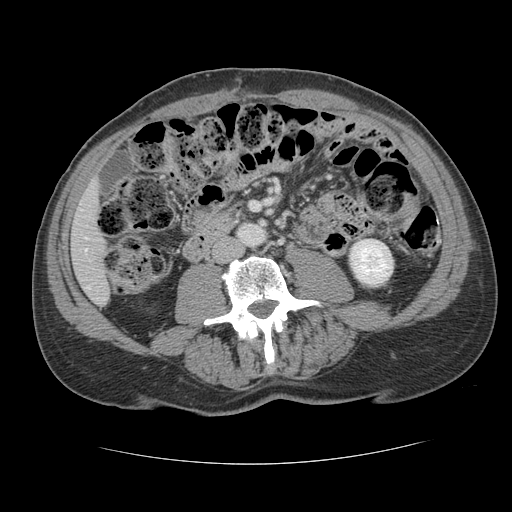
Contrast-enhanced abdominal CT, one axial slice; reconstruction kernel STANDARD; 120 kVp; intravenous contrast given; soft-tissue window (W 400 / L 40 HU); 2.5 mm slice thickness; 512 × 512 image matrix, field of view 377 × 377 mm. Male patient, age 68 years. Case-level facts recorded for this patient, not image findings: diagnosis: colorectal cancer liver metastases, imaged before liver resection; multiple liver metastases: yes; largest metastasis: 2.2 cm; disease in both lobes: no.
Structures marked on this image (expert manual segmentation):
- hepatic veins: bounding box (x1, y1, x2, y2) in pixels: (85, 249, 87, 251)
- liver: (72, 185, 110, 304)
- planned liver remnant (the part of the liver to remain after resection): (72, 185, 110, 304)
- portal vein (with intrahepatic branches): (87, 286, 89, 289)